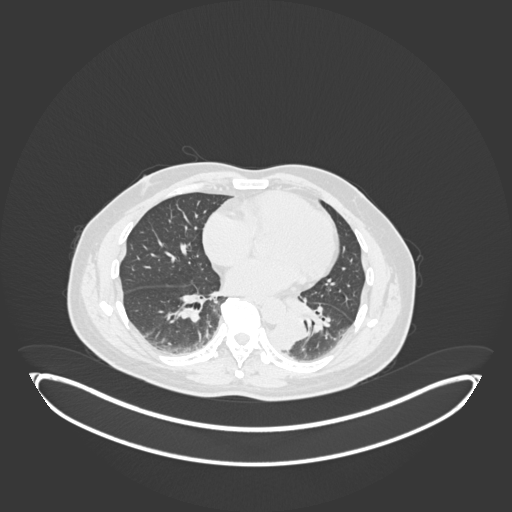
Chest CT, one axial slice. Position 75 of 258 along the scan axis. Reconstruction kernel B30f. 120 kVp. Lung window (W 1500 / L -600 HU). 1 mm slice thickness. 512 × 512 image matrix. Male patient, age 54 years. Case-level facts recorded for this patient, not image findings: clinical TNM (as recorded): T3 N0 M0.
Structures marked on this image (bounding box drawn by a radiologist):
- lung tumour (recorded histology: squamous cell carcinoma): bounding box [x1, y1, x2, y2] px = [273, 305, 311, 350]